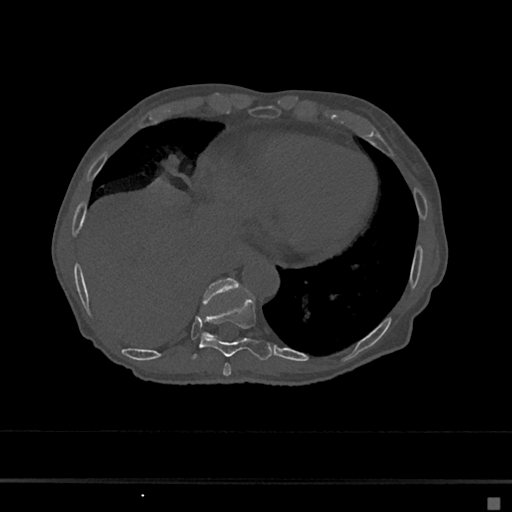
CT including the spine, one axial slice; slice 266 of 797 in the series (ordered by position); reconstruction kernel Br40s/3; 120 kVp; bone window (W 1800 / L 400 HU); 0.5 mm slice thickness; 512 × 512 image matrix, field of view 360 × 360 mm. Female patient, age 68 years. Case-level facts recorded for this patient, not image findings: primary cancer: renal.
Outlined on this slice (semi-automatic segmentation, software-assisted and operator-edited):
- T10 vertebra: box from (x=202, y=278) to (x=241, y=339) px
- T8 vertebra: (x=223, y=363)–(x=231, y=376)
- T9 vertebra: (x=191, y=297)–(x=273, y=361)